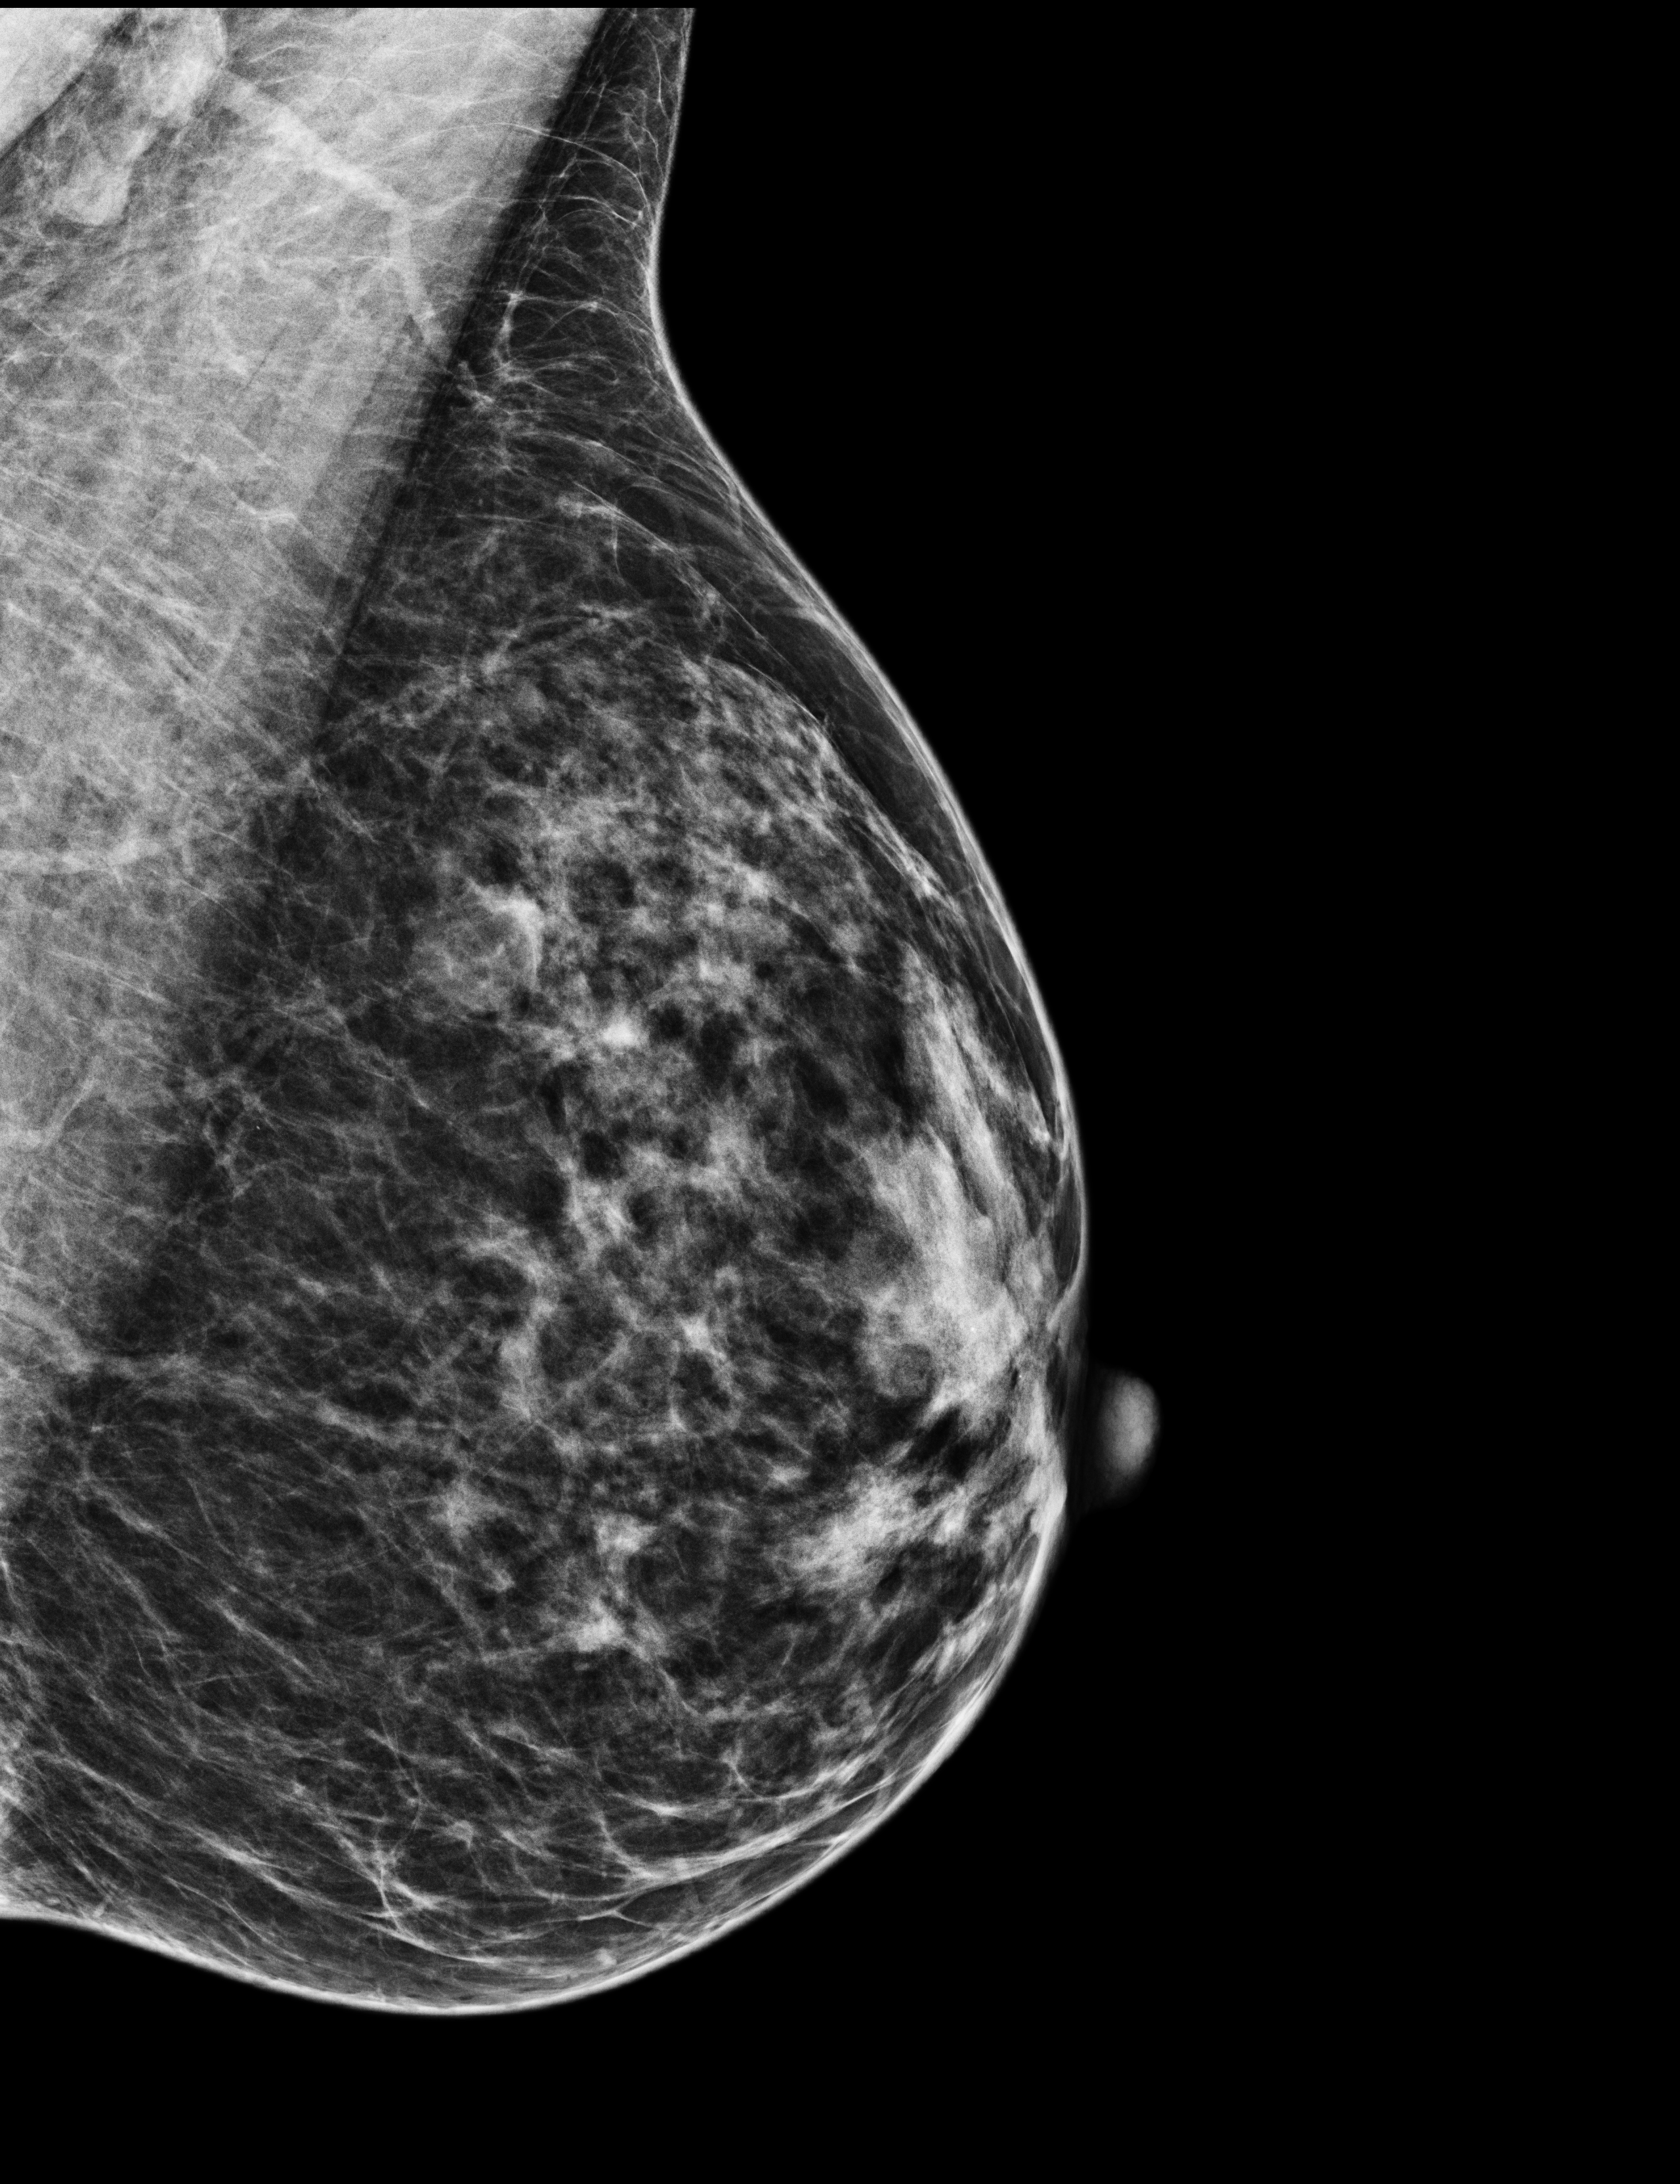
Full-field digital mammogram (FFDM); left breast; mediolateral oblique (MLO) view; screening examination; compressed breast thickness 49 mm; system: Selenia Dimensions. Patient: female, 50 years.
- BI-RADS breast density category at the screening exam (both breasts, scale 1–4): 3
- final BI-RADS assessment for this screening round (tomosynthesis exam, both breasts): category 1
- recall: no recall after this screen